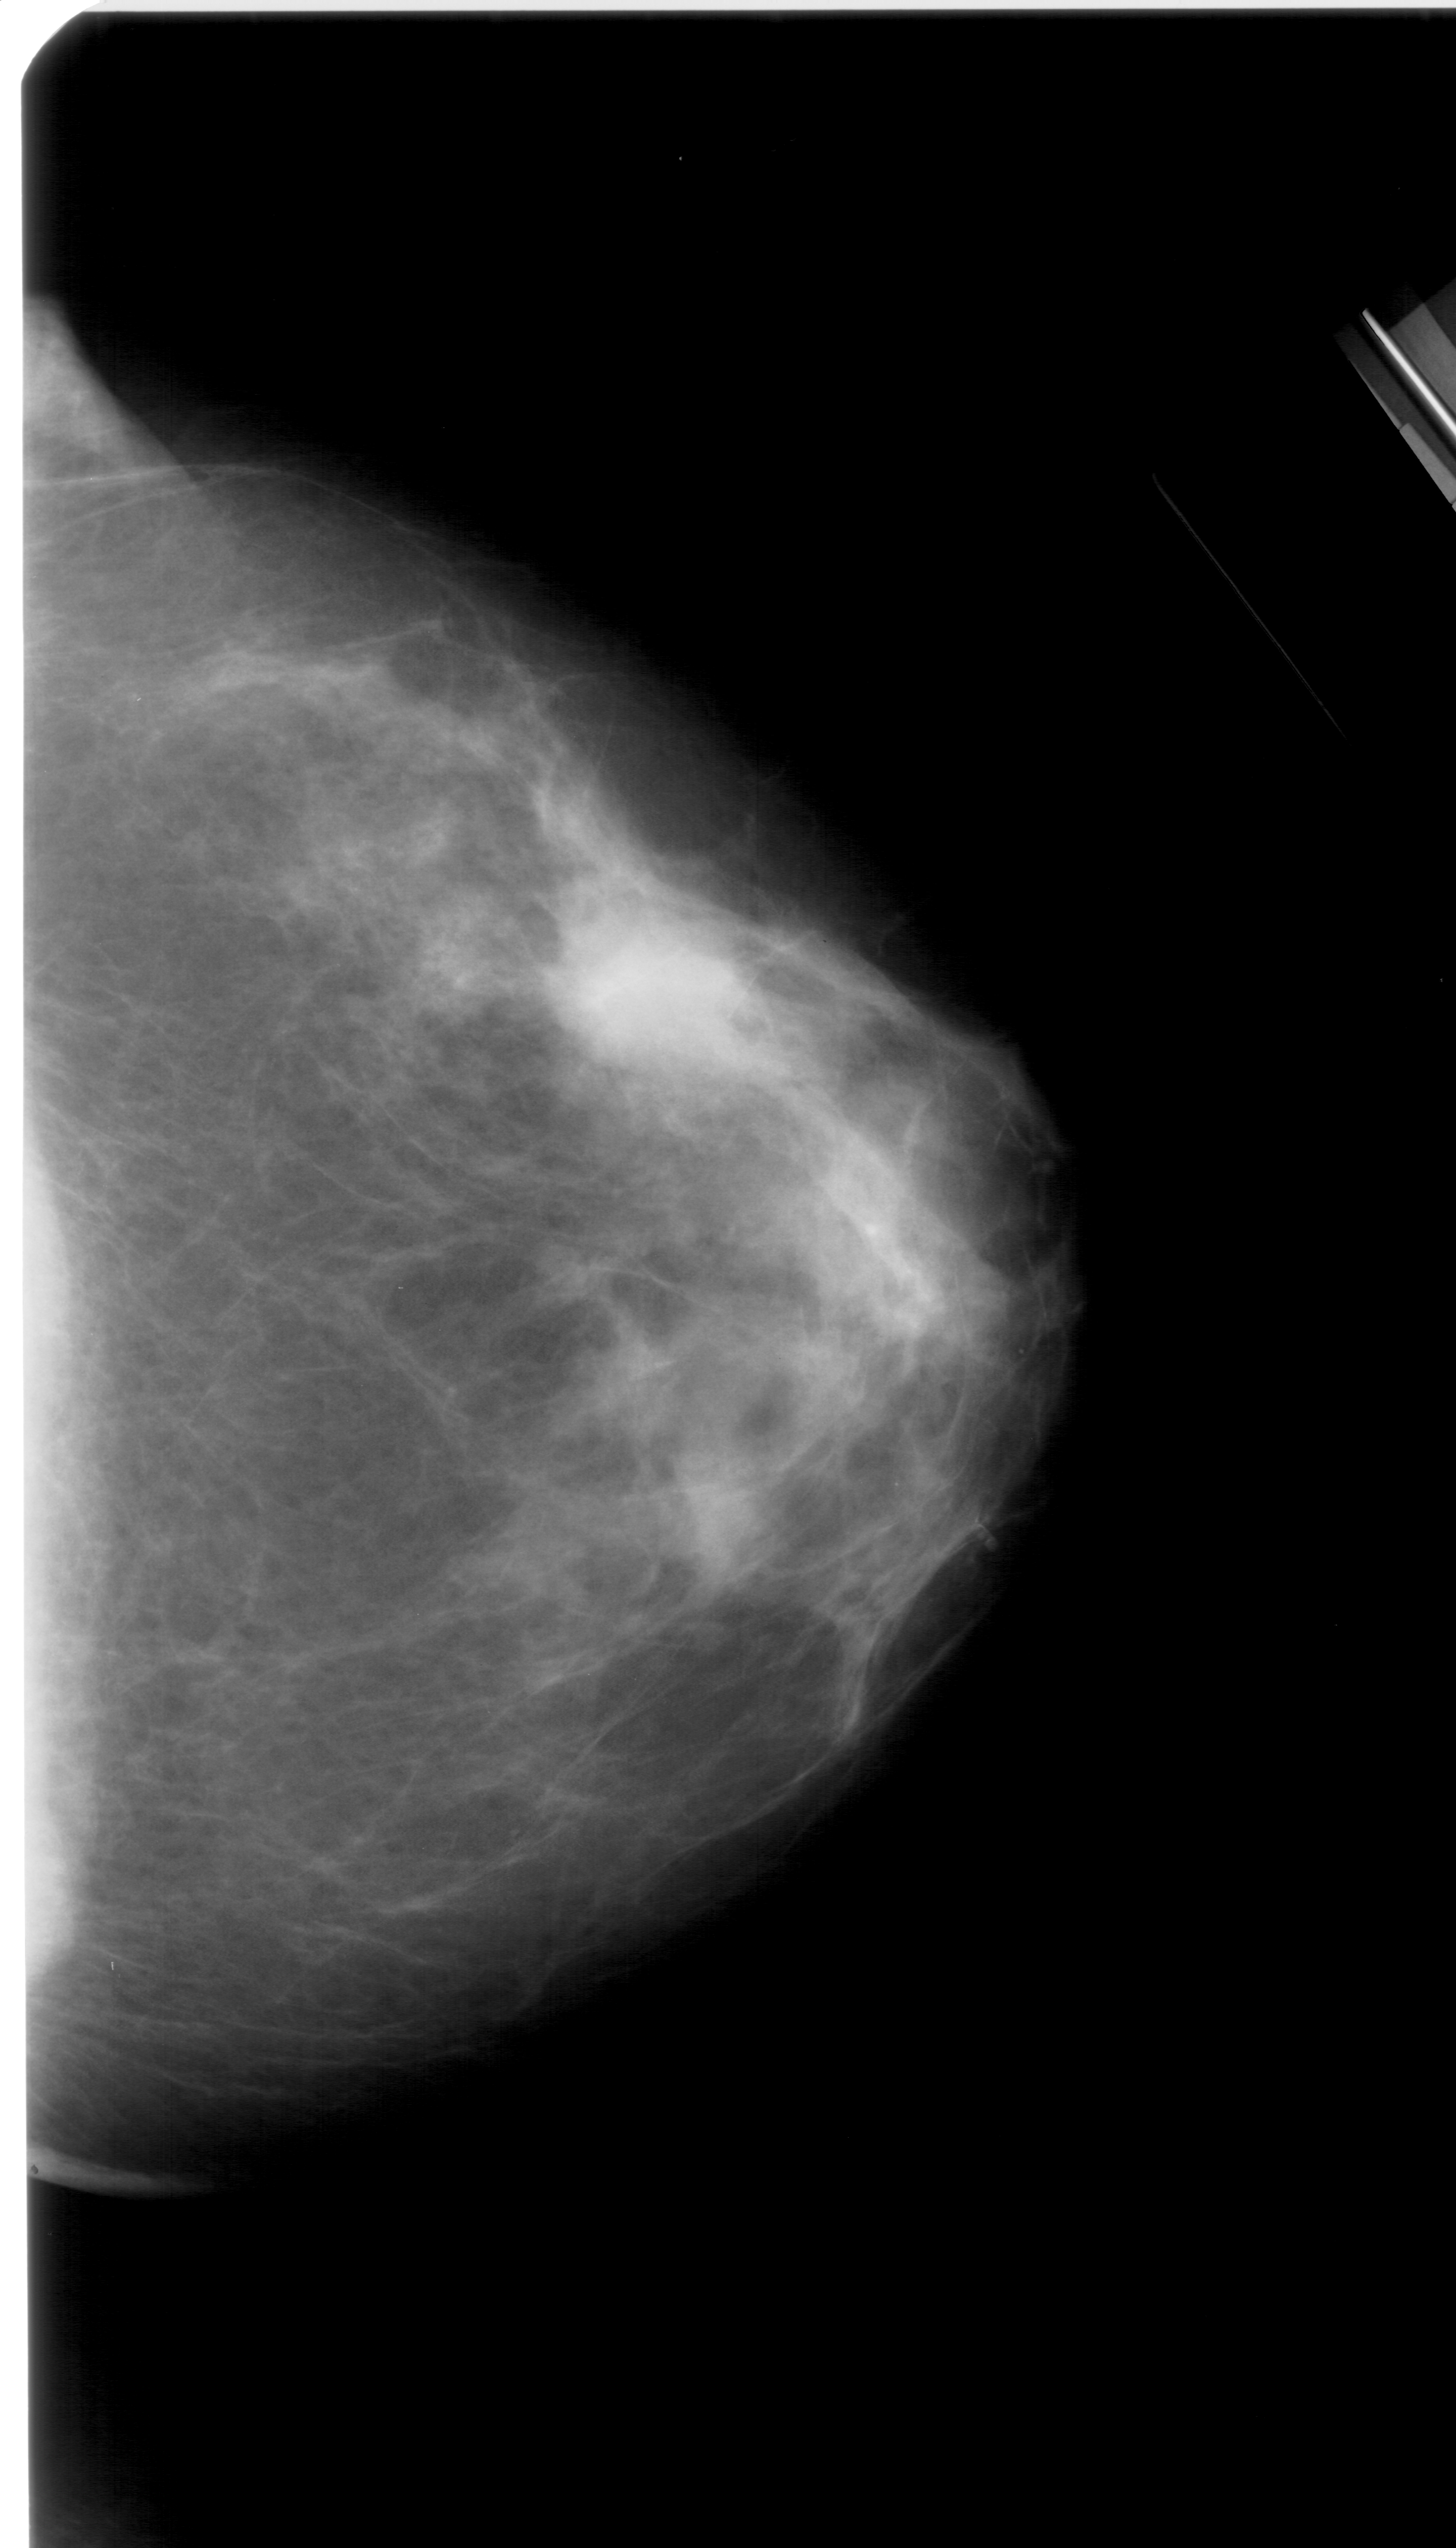
Digitized screen-film mammogram. Right breast. Craniocaudal (CC) view. Breast composition: heterogeneously dense (BI-RADS density category 3 of 4). 1456 × 2548 image matrix.
Expert-marked regions of interest on this image (one box per marked abnormality):
- mass, shape irregular, margins ill defined; BI-RADS assessment category 4; pathology (as recorded): malignant: box from (x=522, y=889) to (x=766, y=1082) px